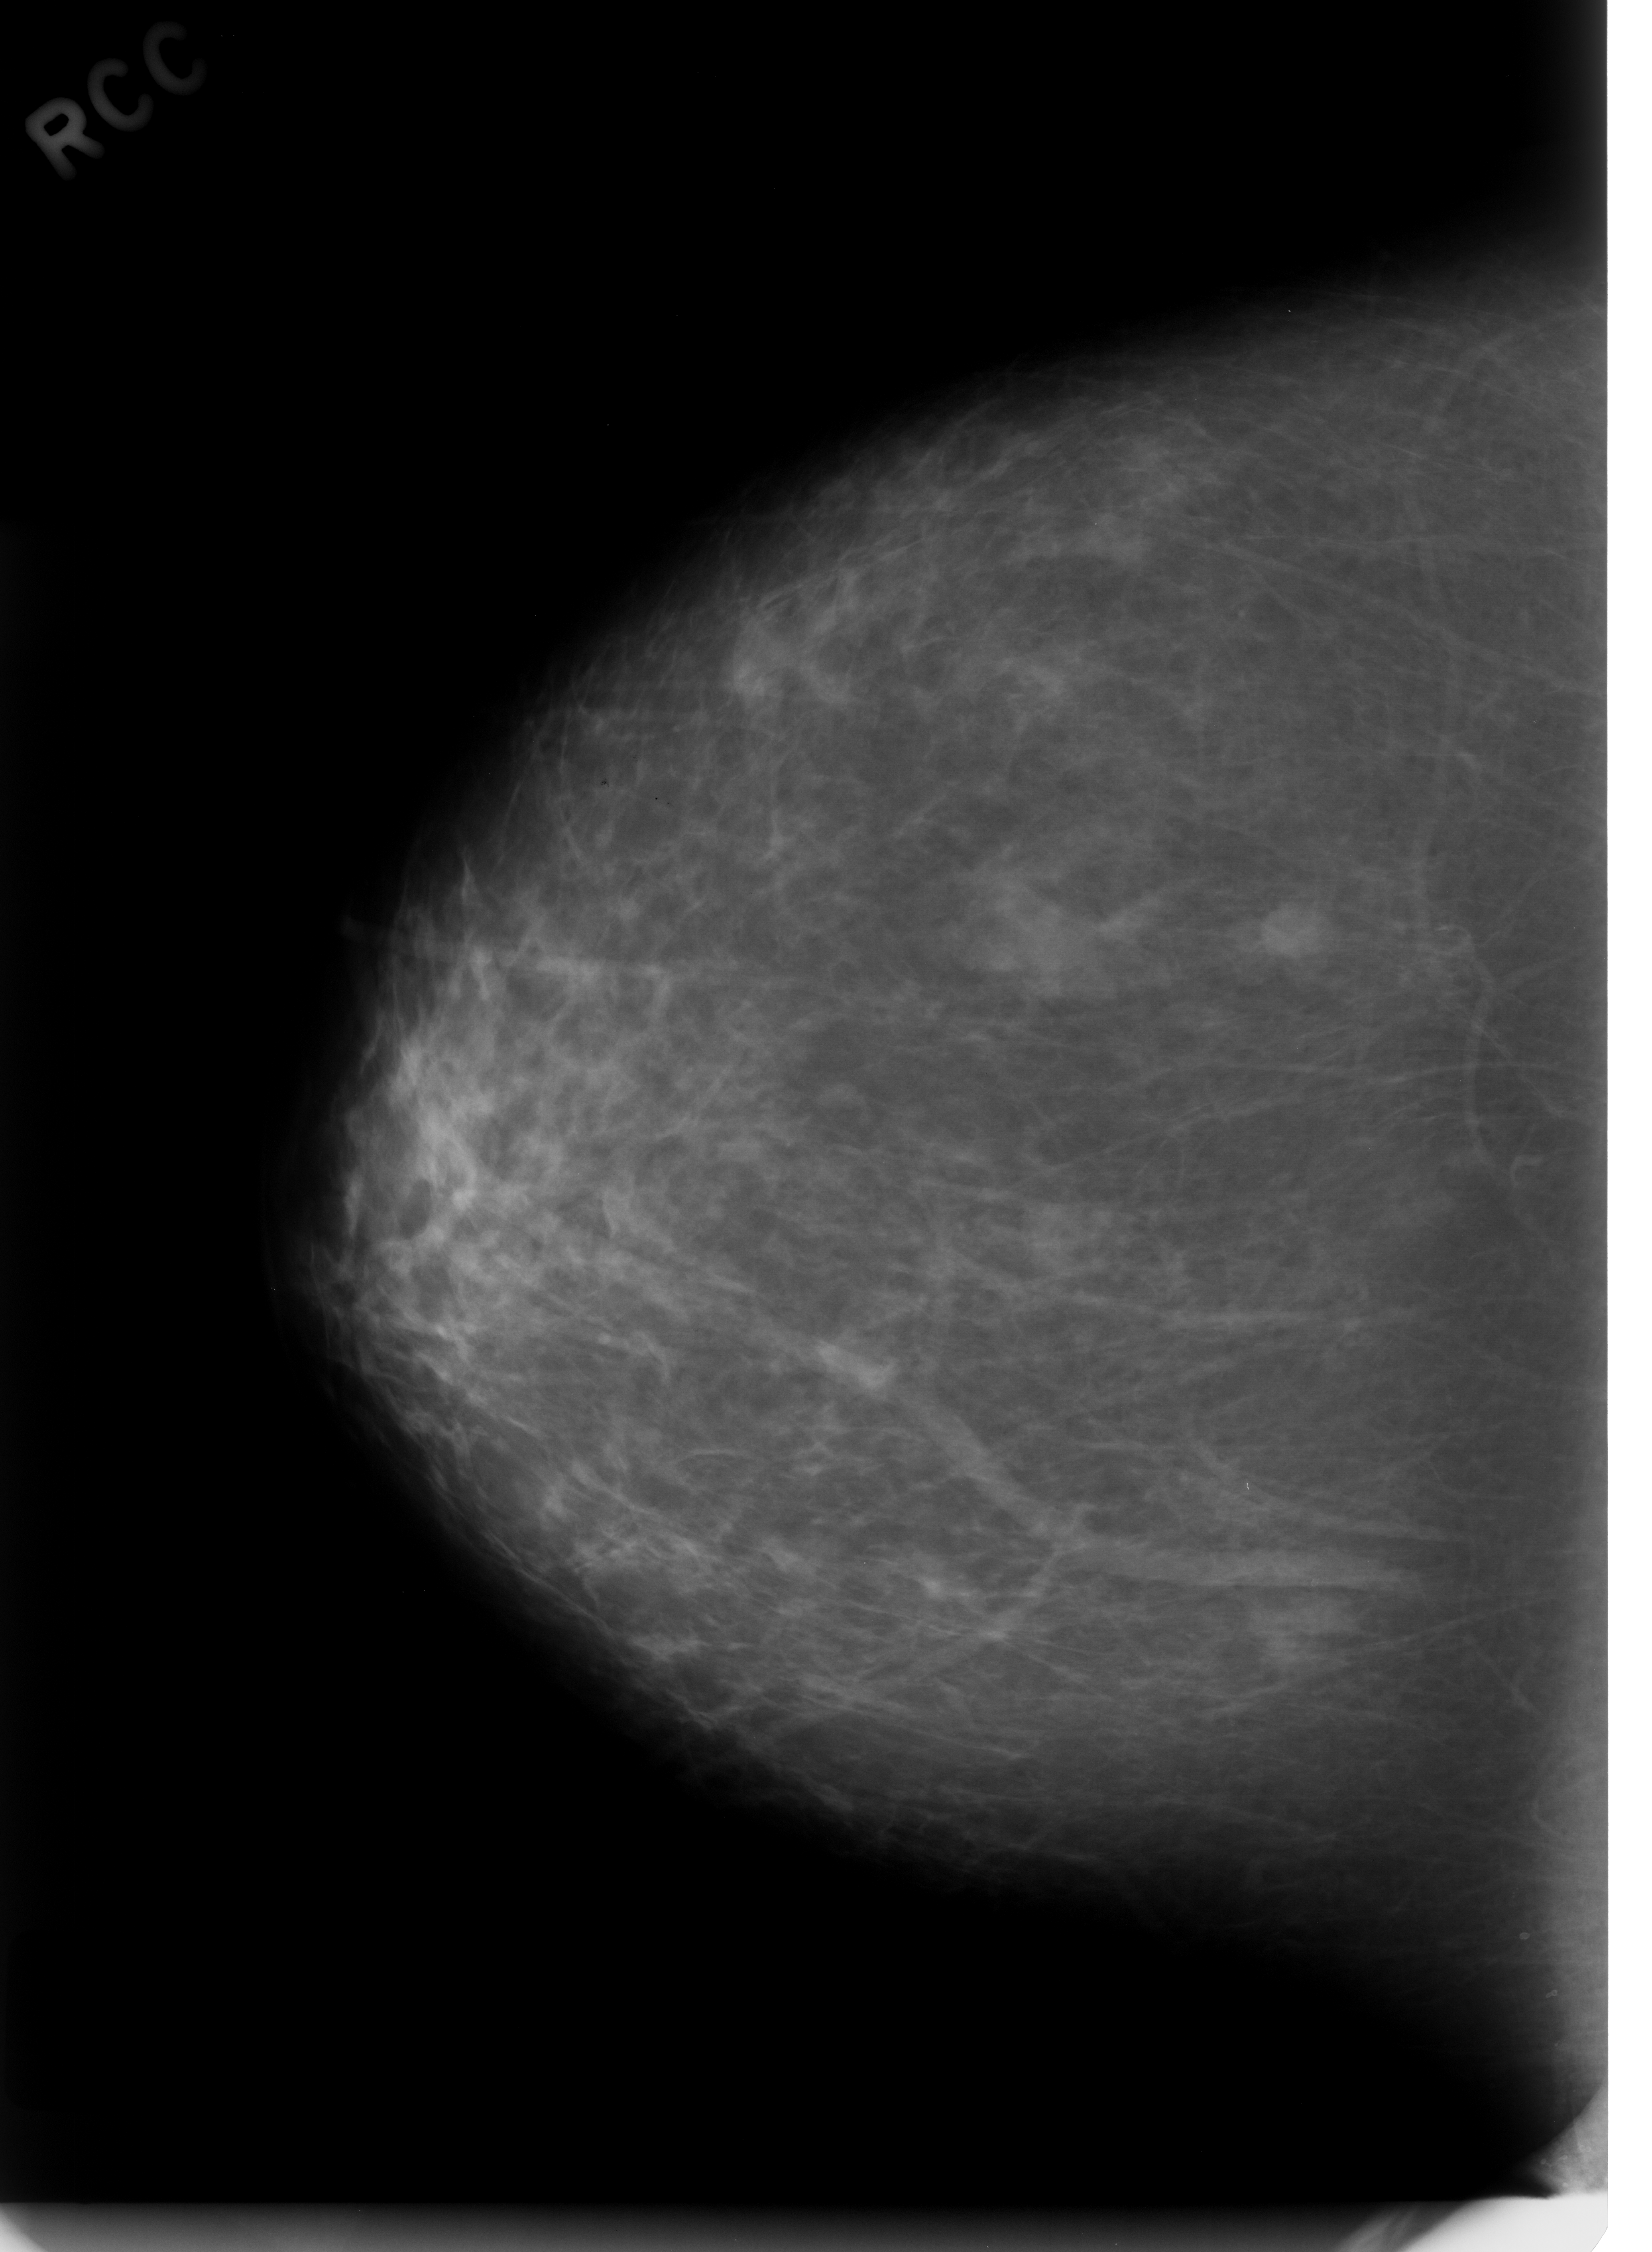
Scanned film-screen mammogram; right breast; CC view; breast composition: almost entirely fatty (BI-RADS density category 1 of 4).
Radiologist-marked abnormalities on this image: mass, shape oval, margins circumscribed; BI-RADS assessment category 3; subtlety rating 5 on a 1 (subtle) to 5 (obvious) scale; pathology (as recorded): benign.